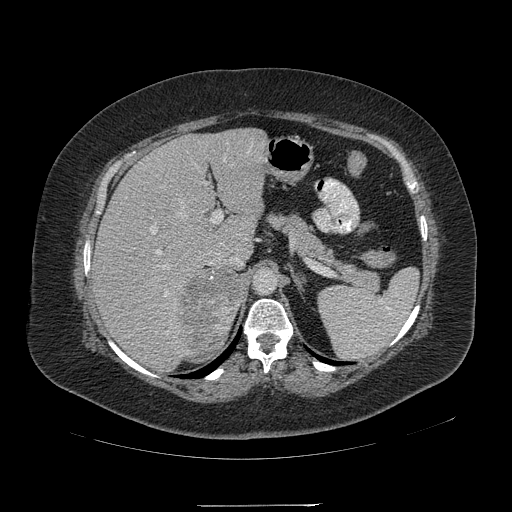
Contrast-enhanced abdominal CT, one axial slice; slice 143 of 217 in the series (ordered by position); reconstruction kernel STANDARD; intravenous contrast given; soft-tissue window (W 400 / L 40 HU); 1.25 mm slice thickness; 512 × 512 image matrix, field of view 453 × 453 mm. Patient: female, 55 years. From the clinical record (not read from this slice): diagnosis: adrenocortical carcinoma; tumour side: right adrenal; tumour size at pathology: 11 cm; Ki-67 index: 20 %; stage (as recorded): 2.
Outlined on this slice (semi-automatically segmented with operator editing):
- mass: bounding box [x1, y1, x2, y2] px = [178, 268, 245, 357]